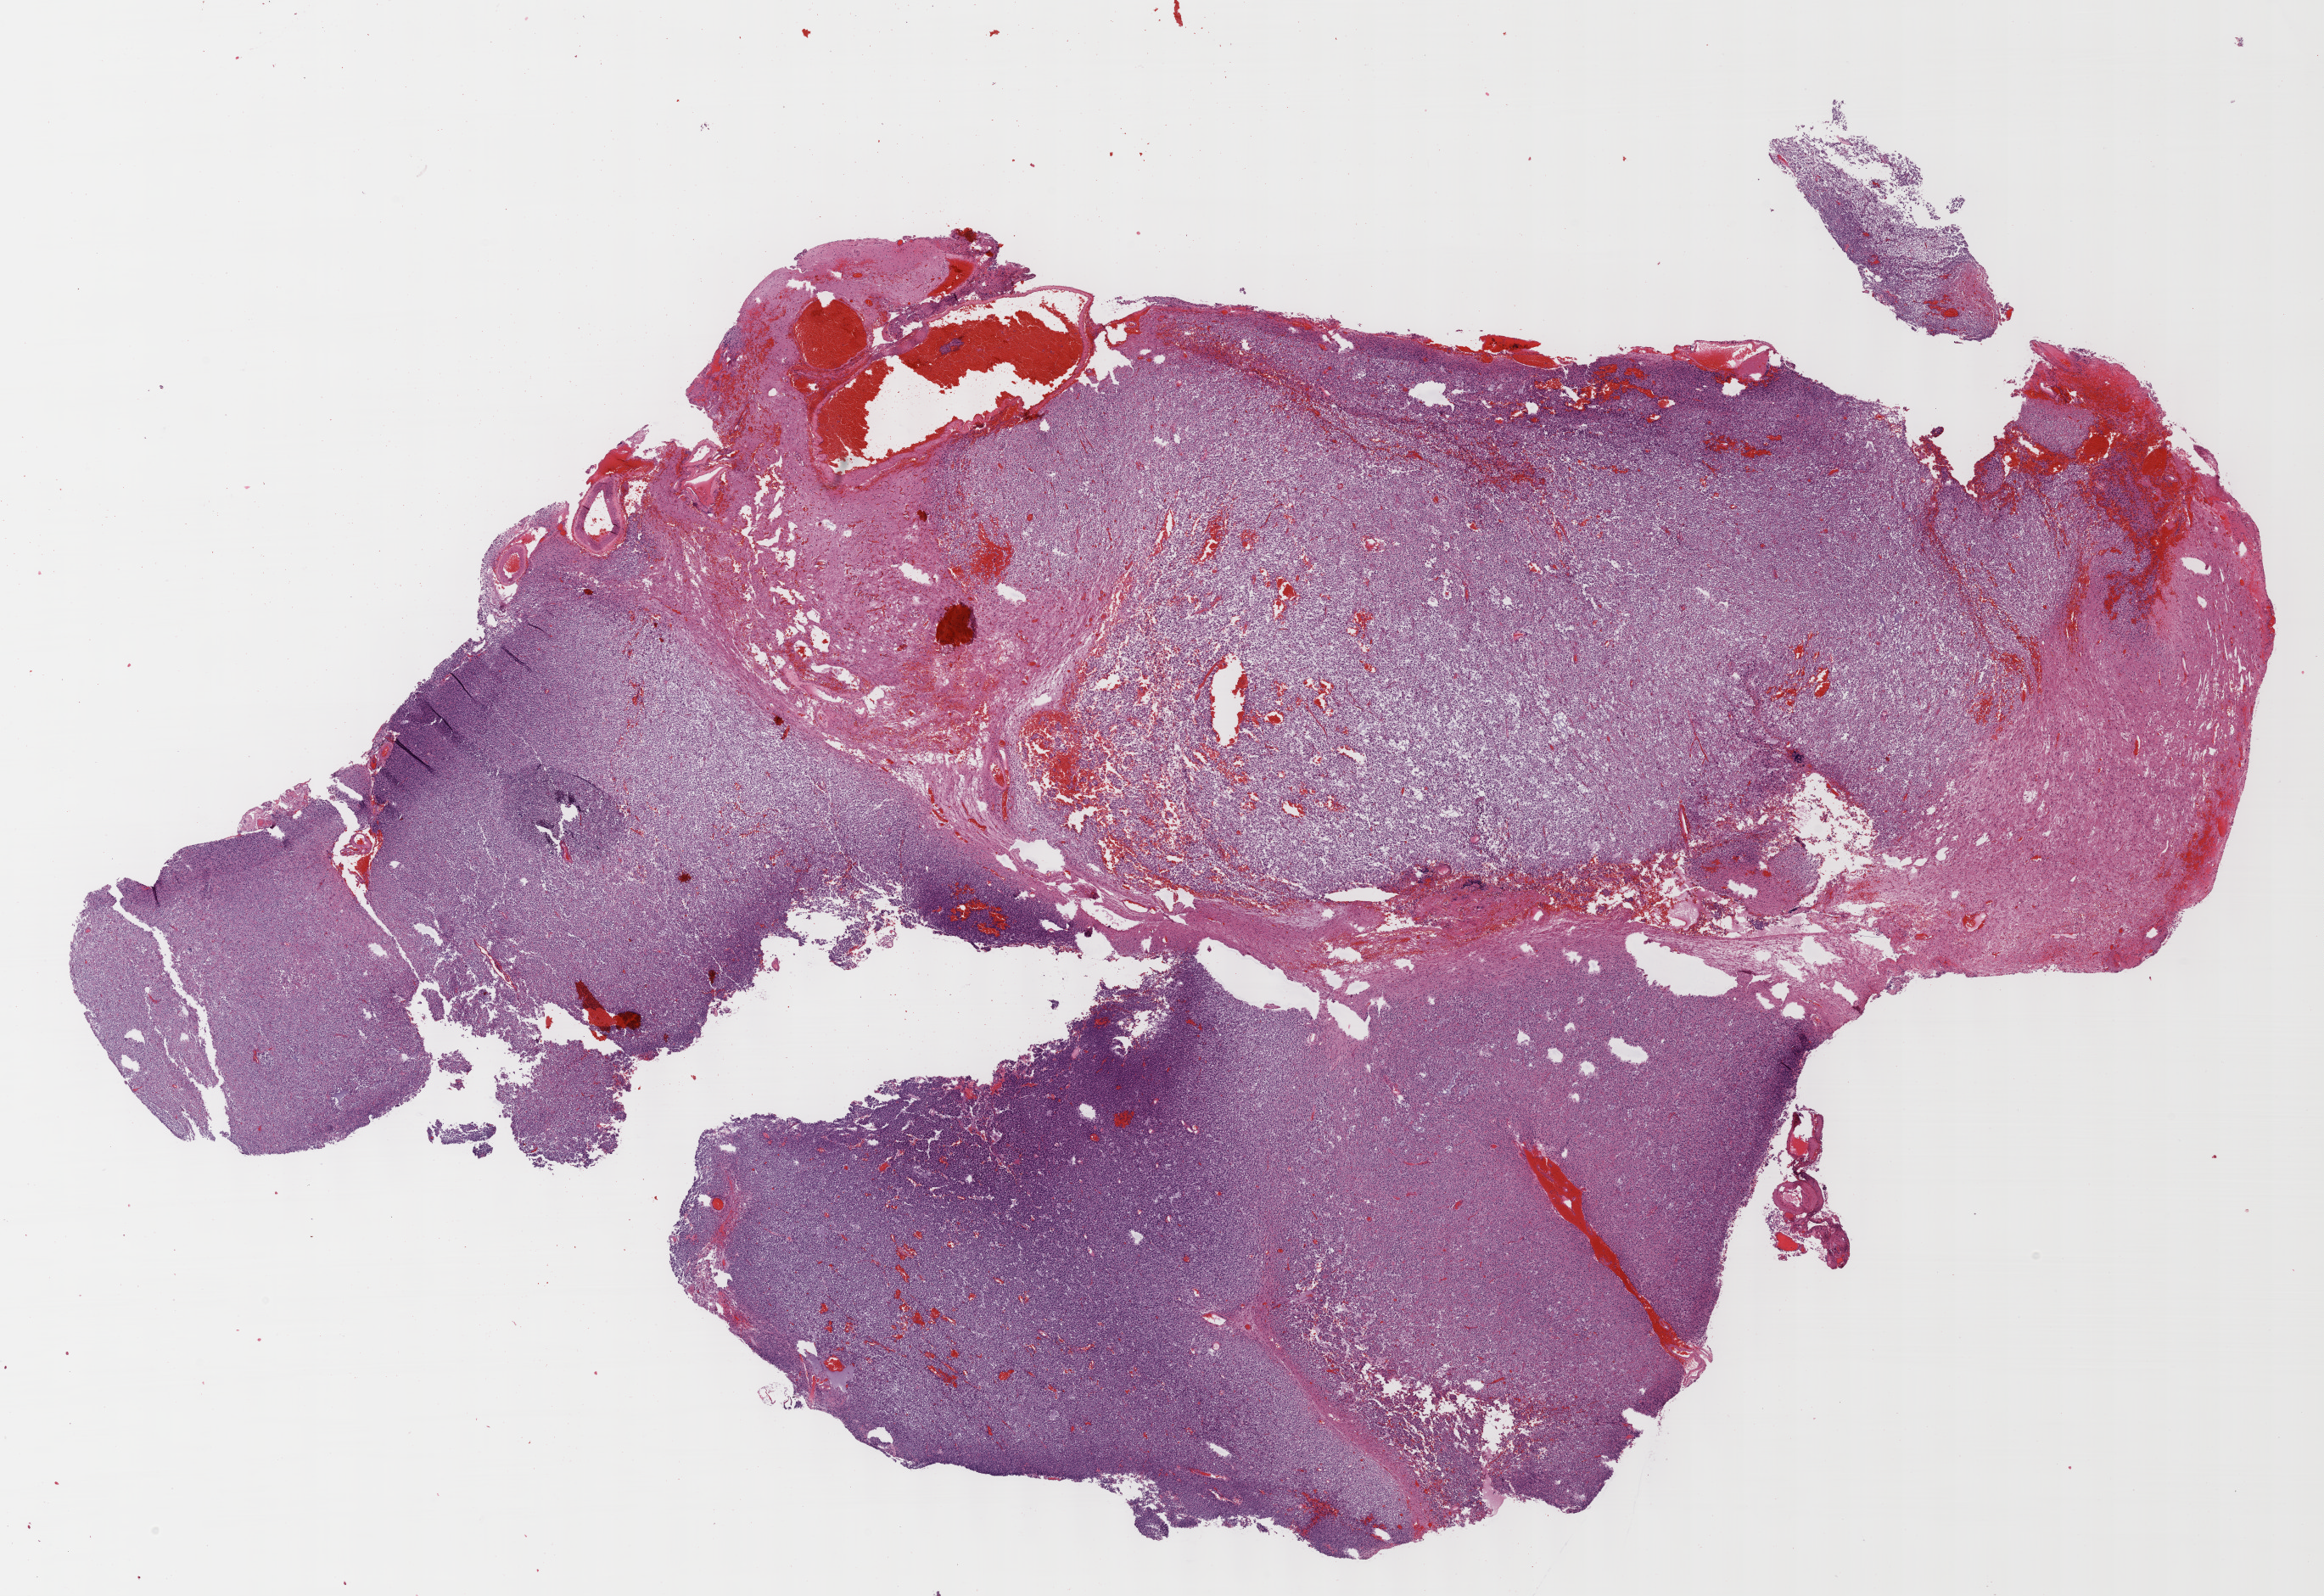
Hematoxylin and eosin (H&E) stained whole-slide image, low-resolution overview of the scanned area, about 22.1 x 15.2 mm (slide scanned at 40x); formalin-fixed paraffin-embedded (FFPE) diagnostic section; brain, primary tumour sample. Female, age 48 years at initial diagnosis. Histologic grade: G3 (poorly differentiated).
* laterality: right
* histologic diagnosis: Oligodendroglioma, anaplastic (cerebrum)